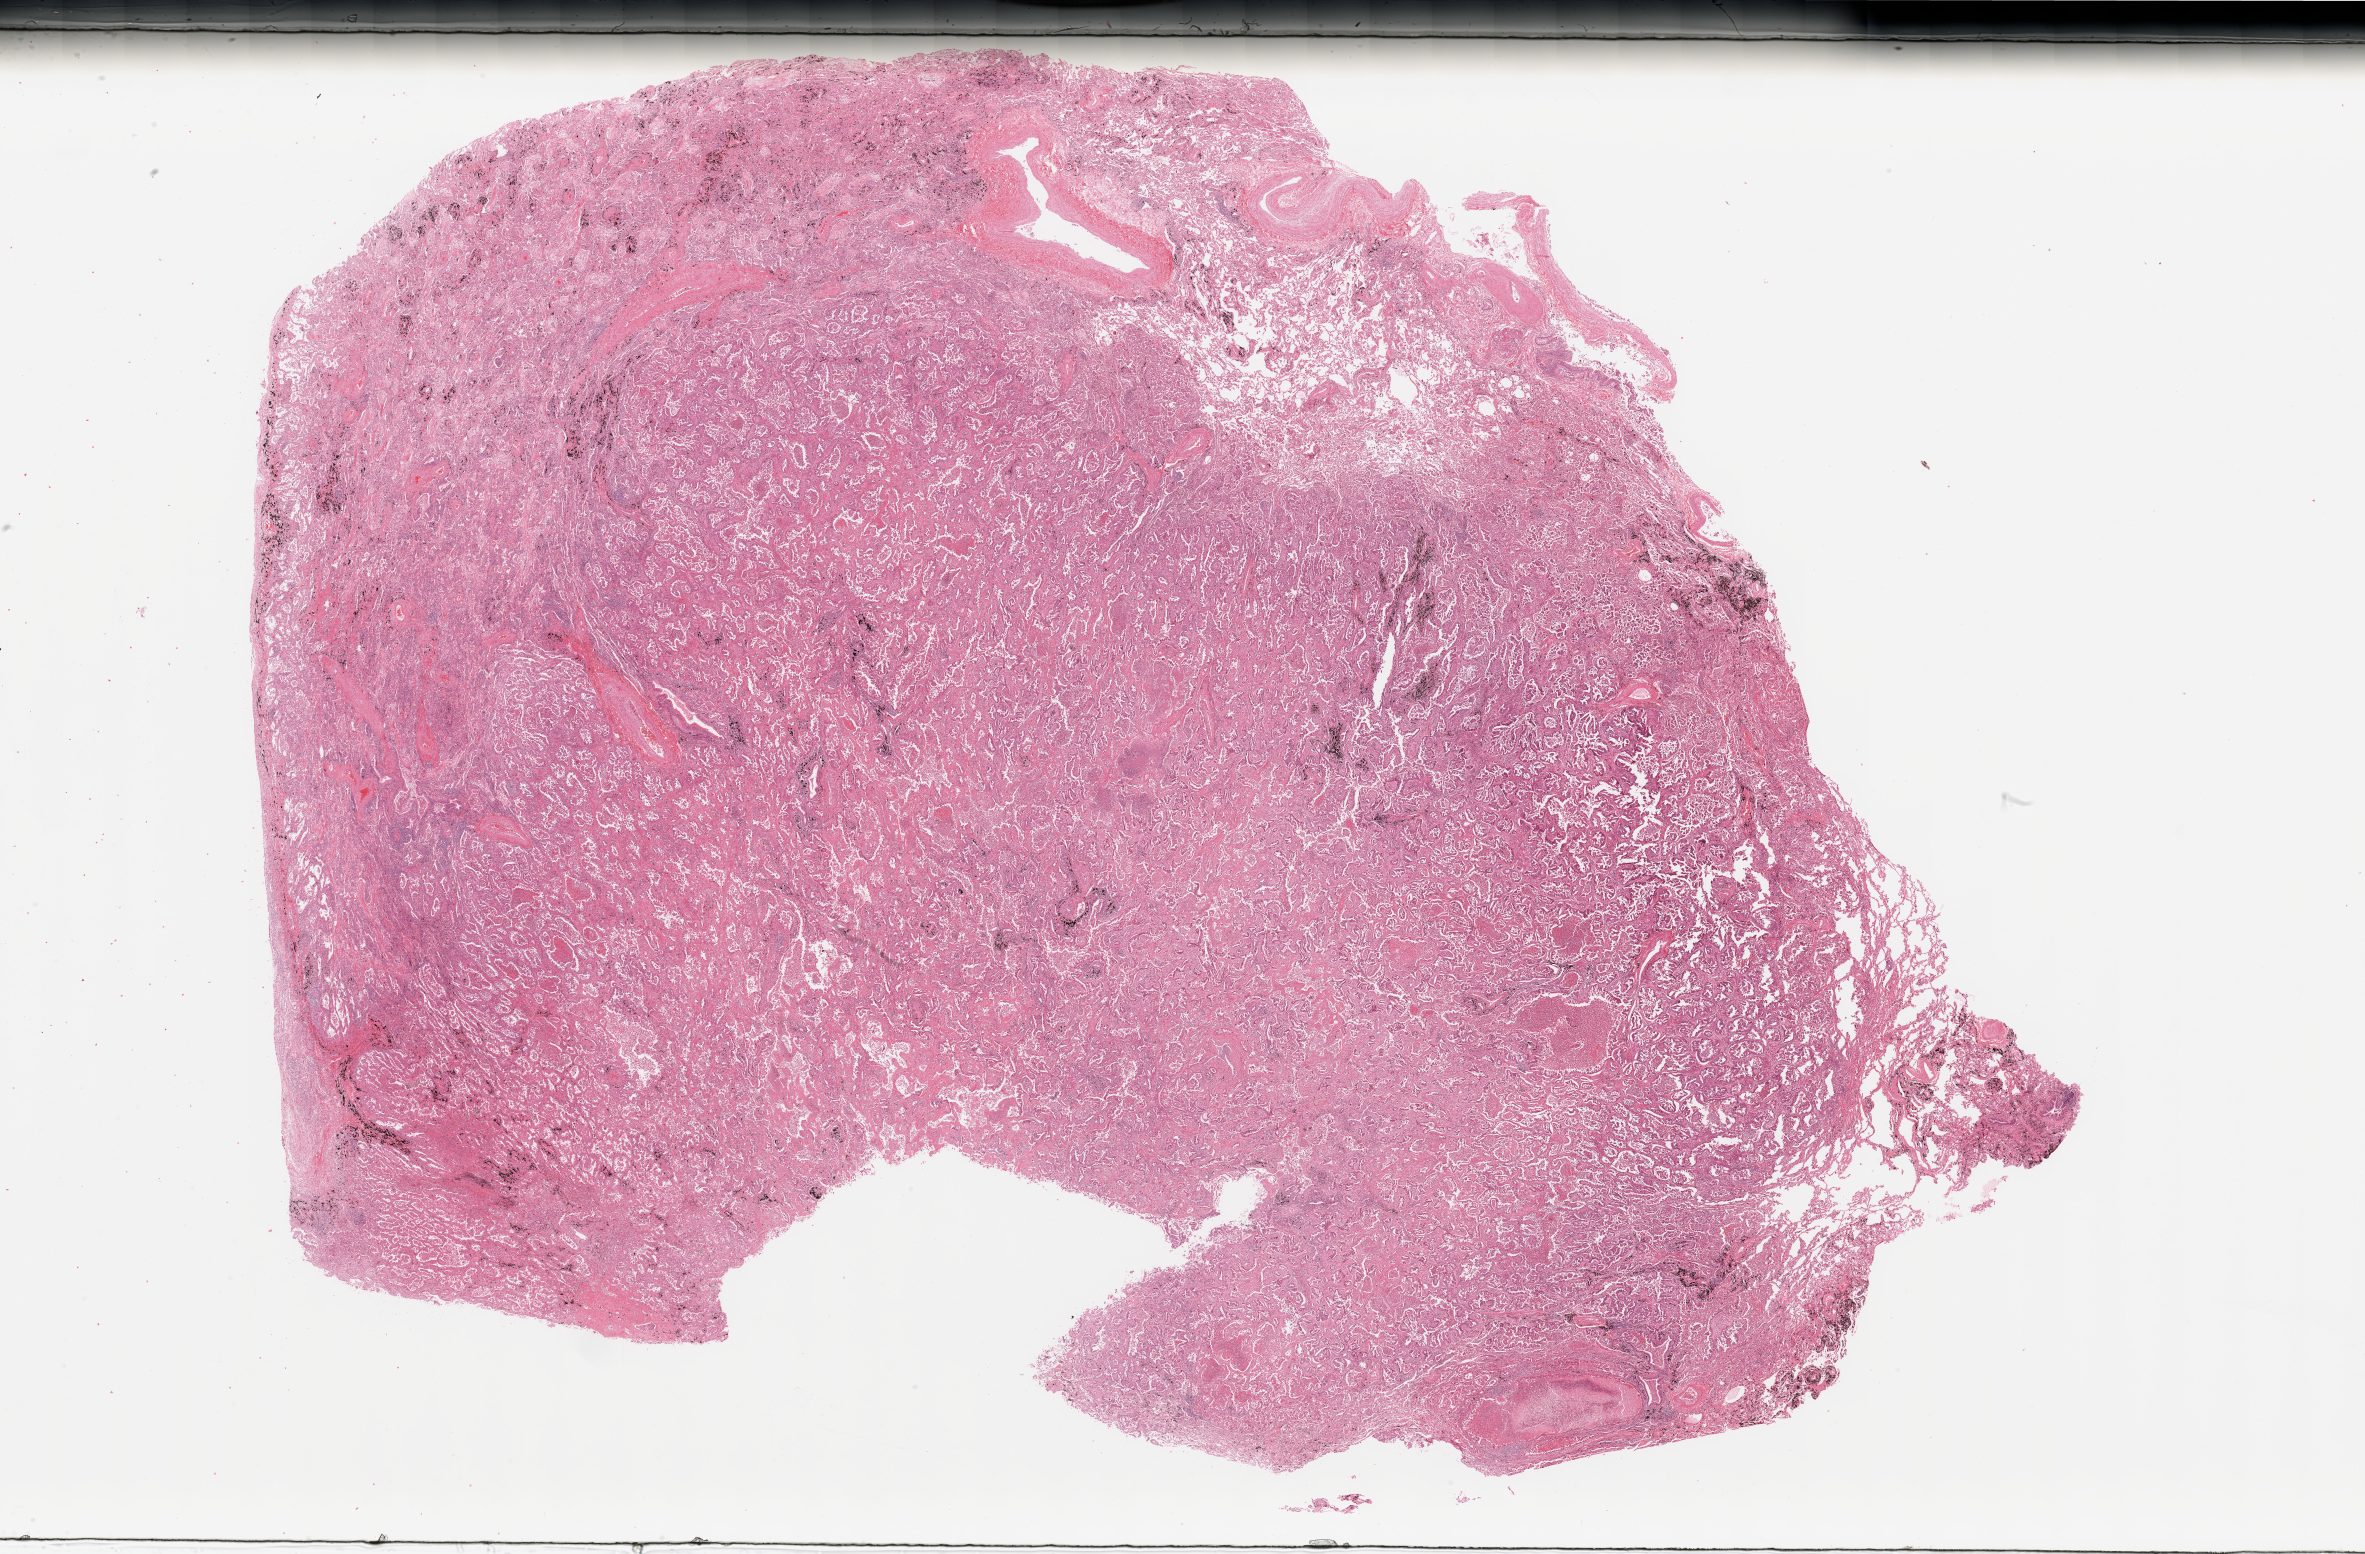
Whole-slide histology image, H&E-stained, whole scanned area (about 37.4 x 24.6 mm, acquisition: 20x scan) shown as a low-resolution overview; tumour tissue sample, lung. Male, 69 y/o. Histologic grade: G2 (moderately differentiated).
Diagnosis: Adenocarcinoma, NOS. AJCC pathologic stage: IB. Primary tumour site (as recorded): left lower lobe.